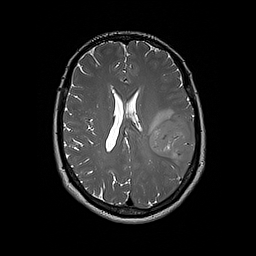
Brain MRI from a brain-tumour surgery series, one axial slice; position 86 of 192 along the scan axis; 1 mm slice thickness; 256 × 256 image matrix. Case-level facts recorded for this patient, not image findings: histopathology: Glioblastoma; WHO grade: 4; IDH mutation: no.
Outlined on this slice (manually delineated by an expert):
- tumour: bounding box (x1, y1, x2, y2) in pixels: (150, 115, 195, 165)